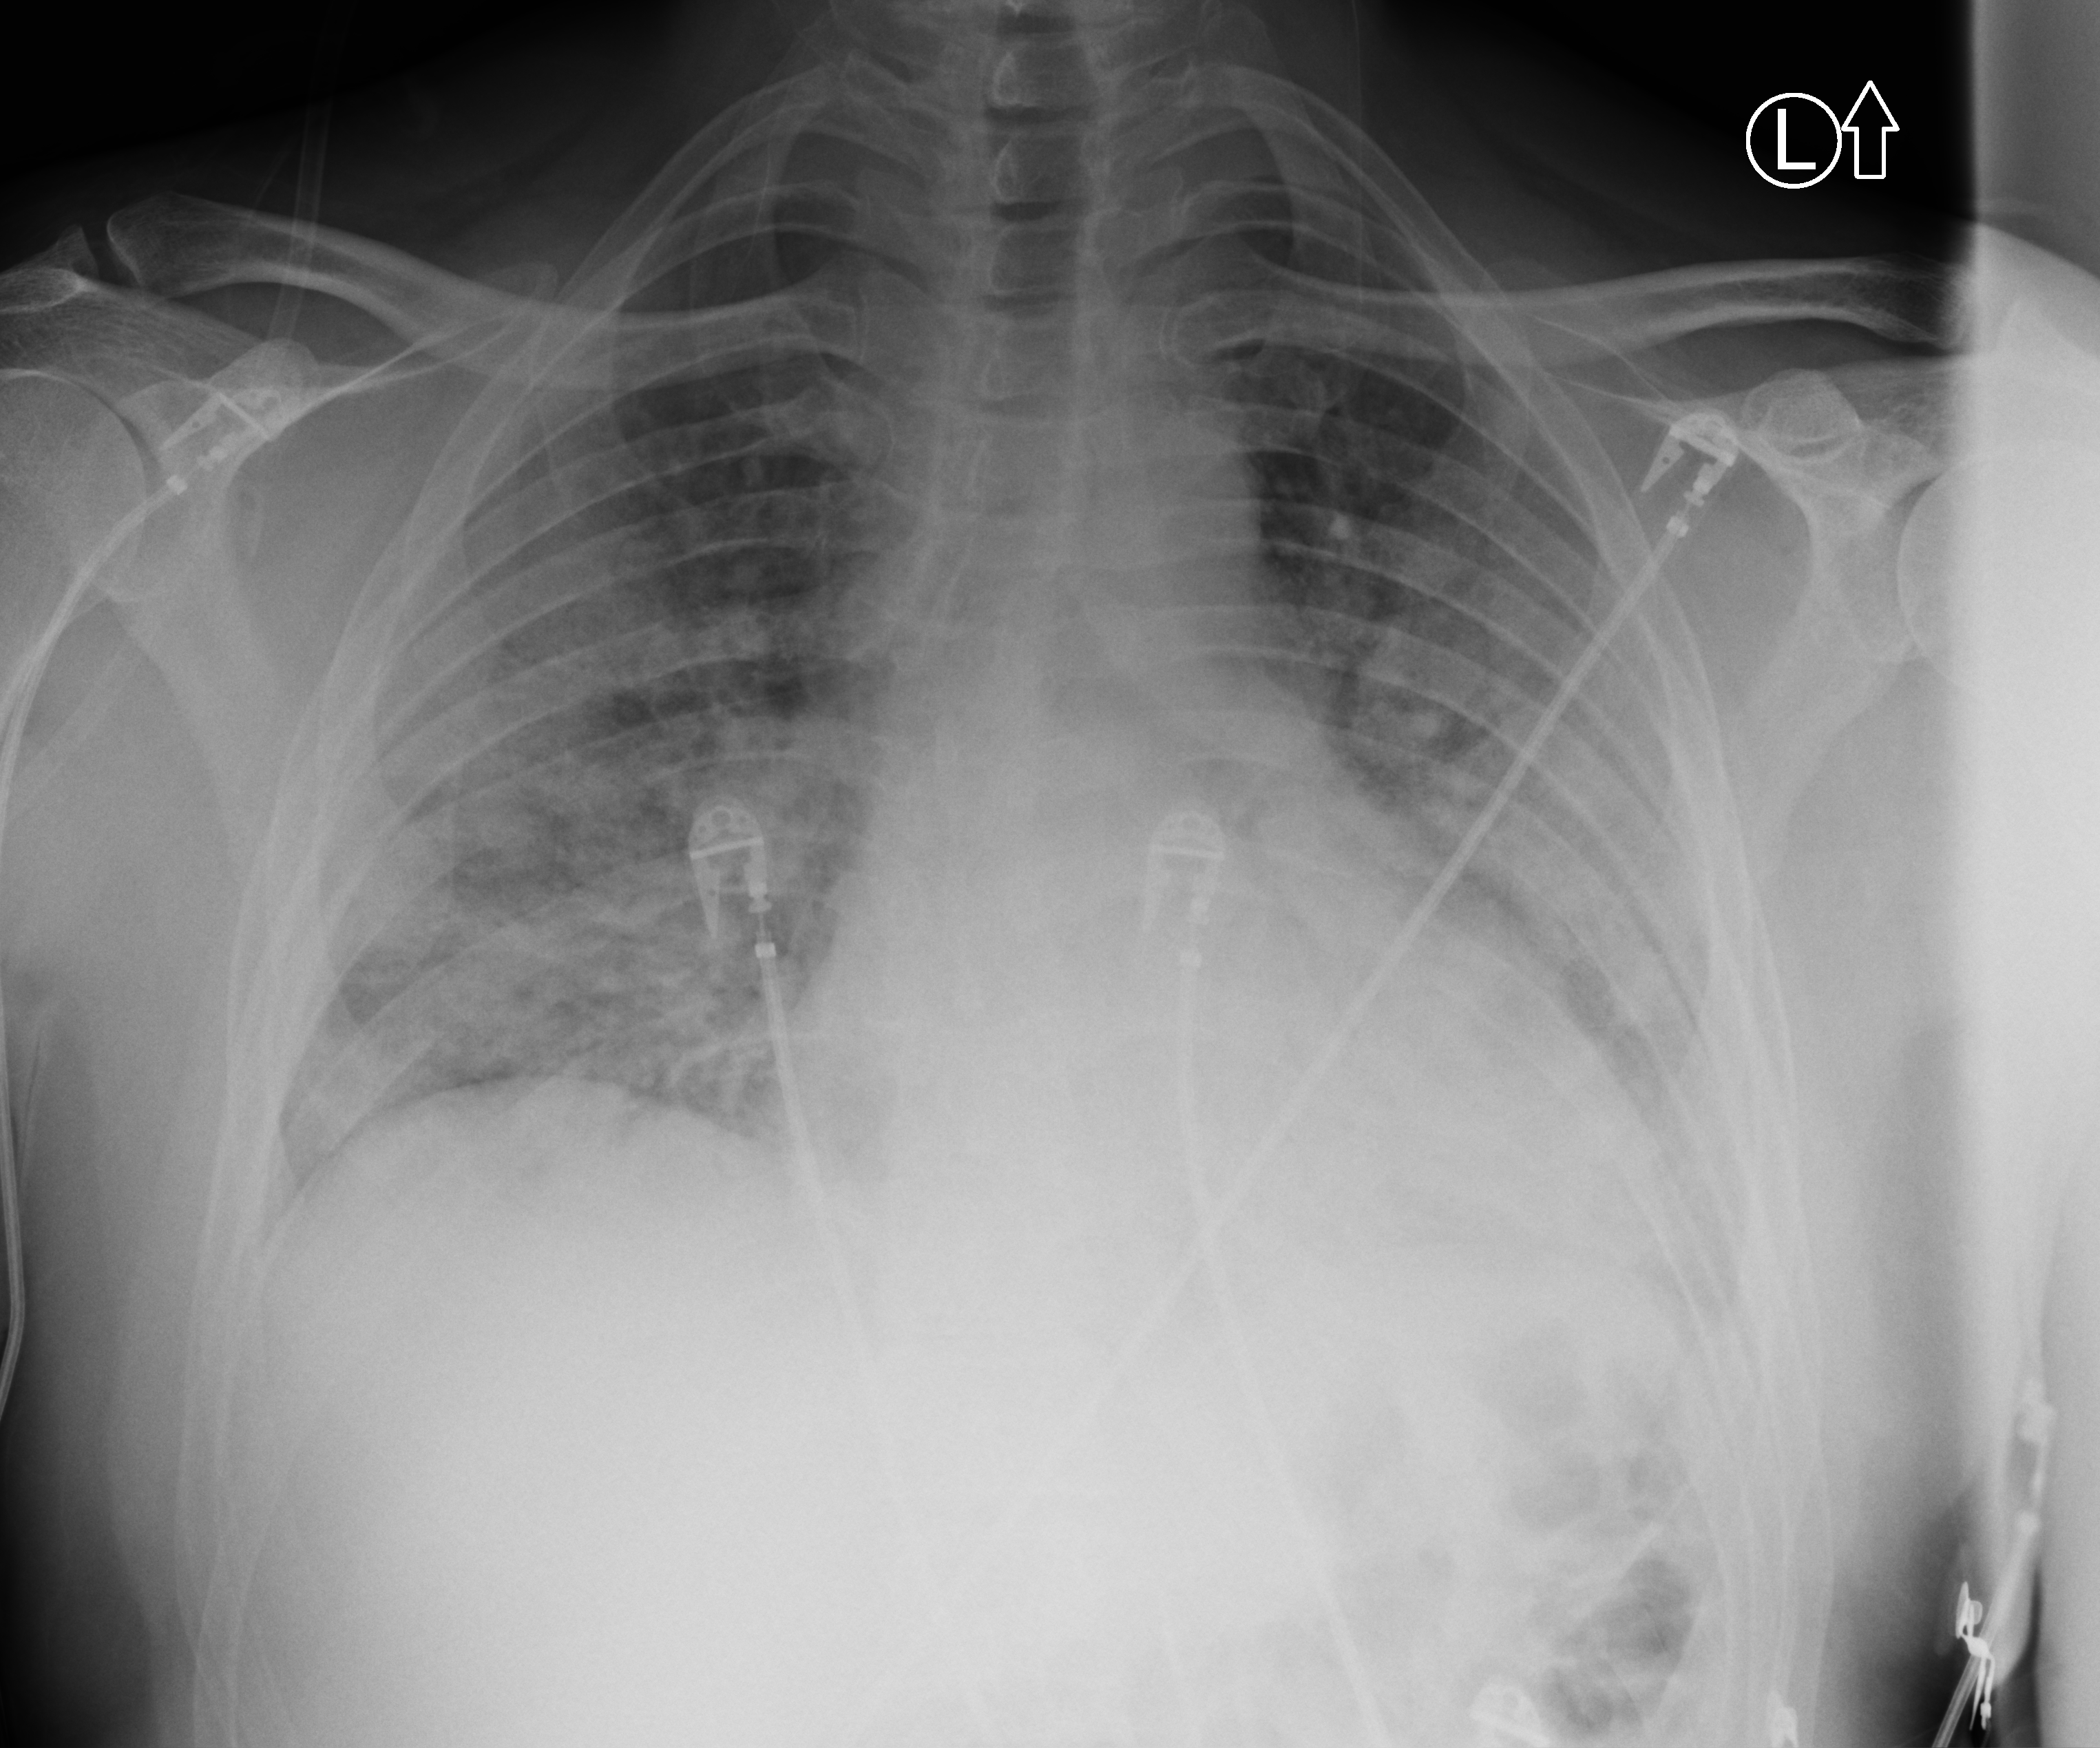
Bedside chest radiograph (computed radiography), anteroposterior (AP) projection. Patient hospitalised with COVID-19; male, aged 18–59 years.
Admission-level facts for this patient (not findings on this image; timing relative to this image not recorded): admitted to intensive care during this hospital stay: yes.